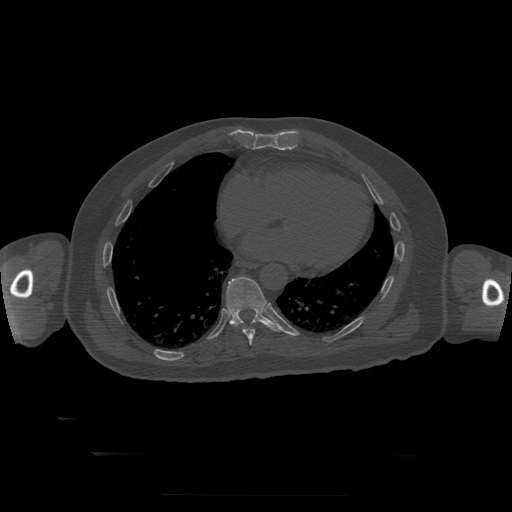
CT including the spine, one axial slice. Slice 133 of 397 in the series (ordered by position). Reconstruction kernel STANDARD. Bone window (W 1800 / L 400 HU). 1.25 mm slice thickness. 512 × 512 image matrix. Patient age 73 years. Case-level facts recorded for this patient, not image findings: primary cancer: prostate.
Outlined on this slice (semi-automatic segmentation, software-assisted and operator-edited):
- T10 vertebra: bounding box <226,277,284,332> (left, top, right, bottom; pixels)
- T9 vertebra: <243,328,256,346>